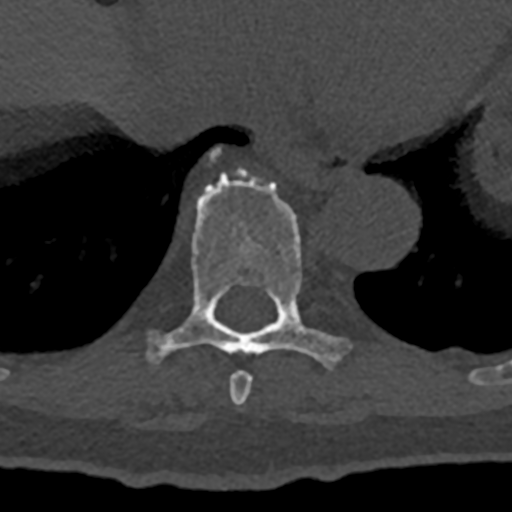
CT including the spine, one axial slice. Reconstruction kernel Br40s/3. 120 kVp. Bone window (W 1800 / L 400 HU). 0.5 mm slice thickness. 512 × 512 image matrix, field of view 160 × 160 mm. Patient: male, 74 years. From the clinical record (not read from this slice): primary cancer: renal; vertebrae with lytic lesions (as recorded): T10, L1, L2, L3, L4, L5.
Structures marked on this image (semi-automatic segmentation, software-assisted and operator-edited):
- T8 vertebra: box from (x=229, y=371) to (x=252, y=405) px
- T9 vertebra: (x=147, y=149)–(x=351, y=369)